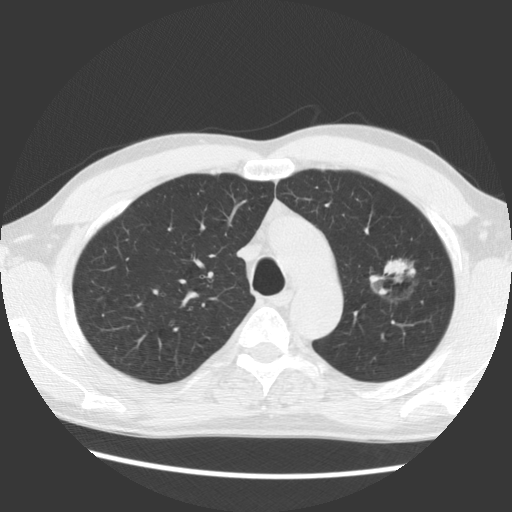
Low-dose screening chest CT, axial slice; baseline screening round; lung window (W 1500 / L -600 HU); standard (soft-tissue) reconstruction kernel (STANDARD); slice 101 of 138 in the series. Male participant, aged 61 years at enrolment. Former smoker at enrolment.
- Expert reader's lesion annotation, bounding box (x1, y1, x2, y2) in pixels: (354, 240, 439, 317).
- Reader record for this screening exam (exam-level; its link to the box is not recorded): non-calcified nodule or mass ≥4 mm, left upper lobe, 17 × 14 mm, soft tissue attenuation.
- Official screen result: positive, change unspecified: nodule(s) >= 4 mm or enlarging nodule(s), mass(es), or other non-specific abnormalities suspicious for lung cancer.
- Participant outcome: lung cancer diagnosed 1061 days after this screen — bronchiolo-alveolar adenocarcinoma, NOS, left upper lobe, well differentiated (G1), stage IB (AJCC 6th edition), 44 mm at pathology.